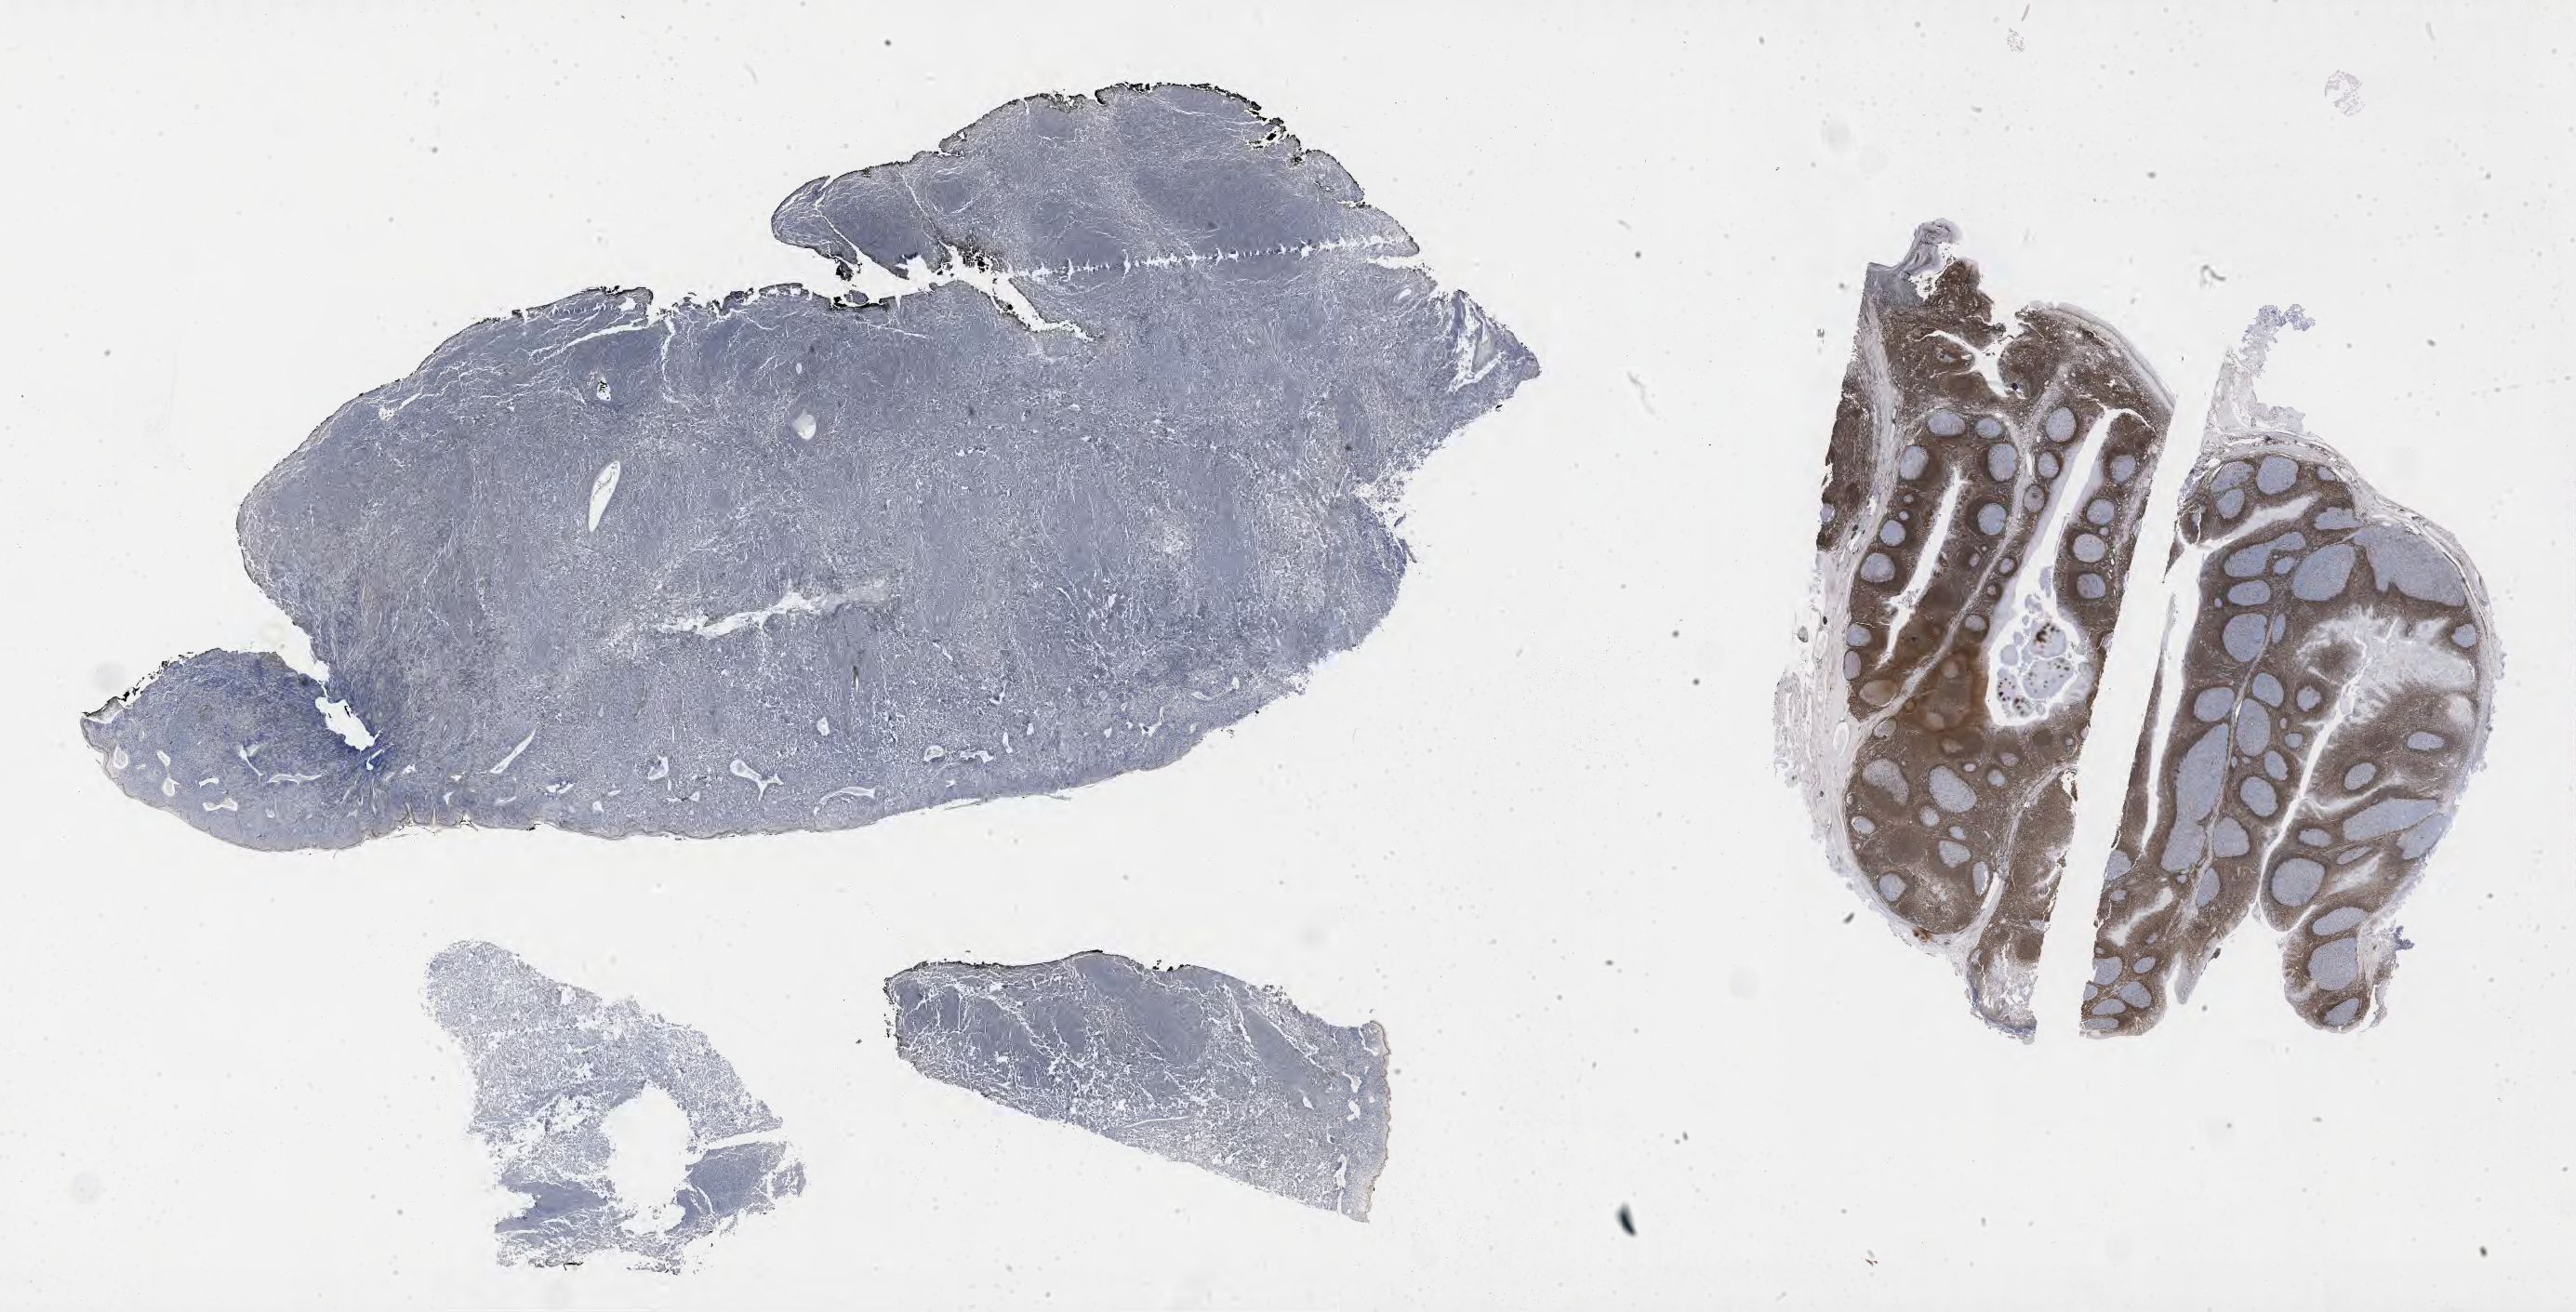
Whole-slide image, immunohistochemical stain for BCL2 — shown as a low-resolution overview of the whole scanned area (about 44.8 x 22.8 mm); specimen: tumor tissue. Patient male; aged 46.
Histologic diagnosis: Burkitt lymphoma, NOS.